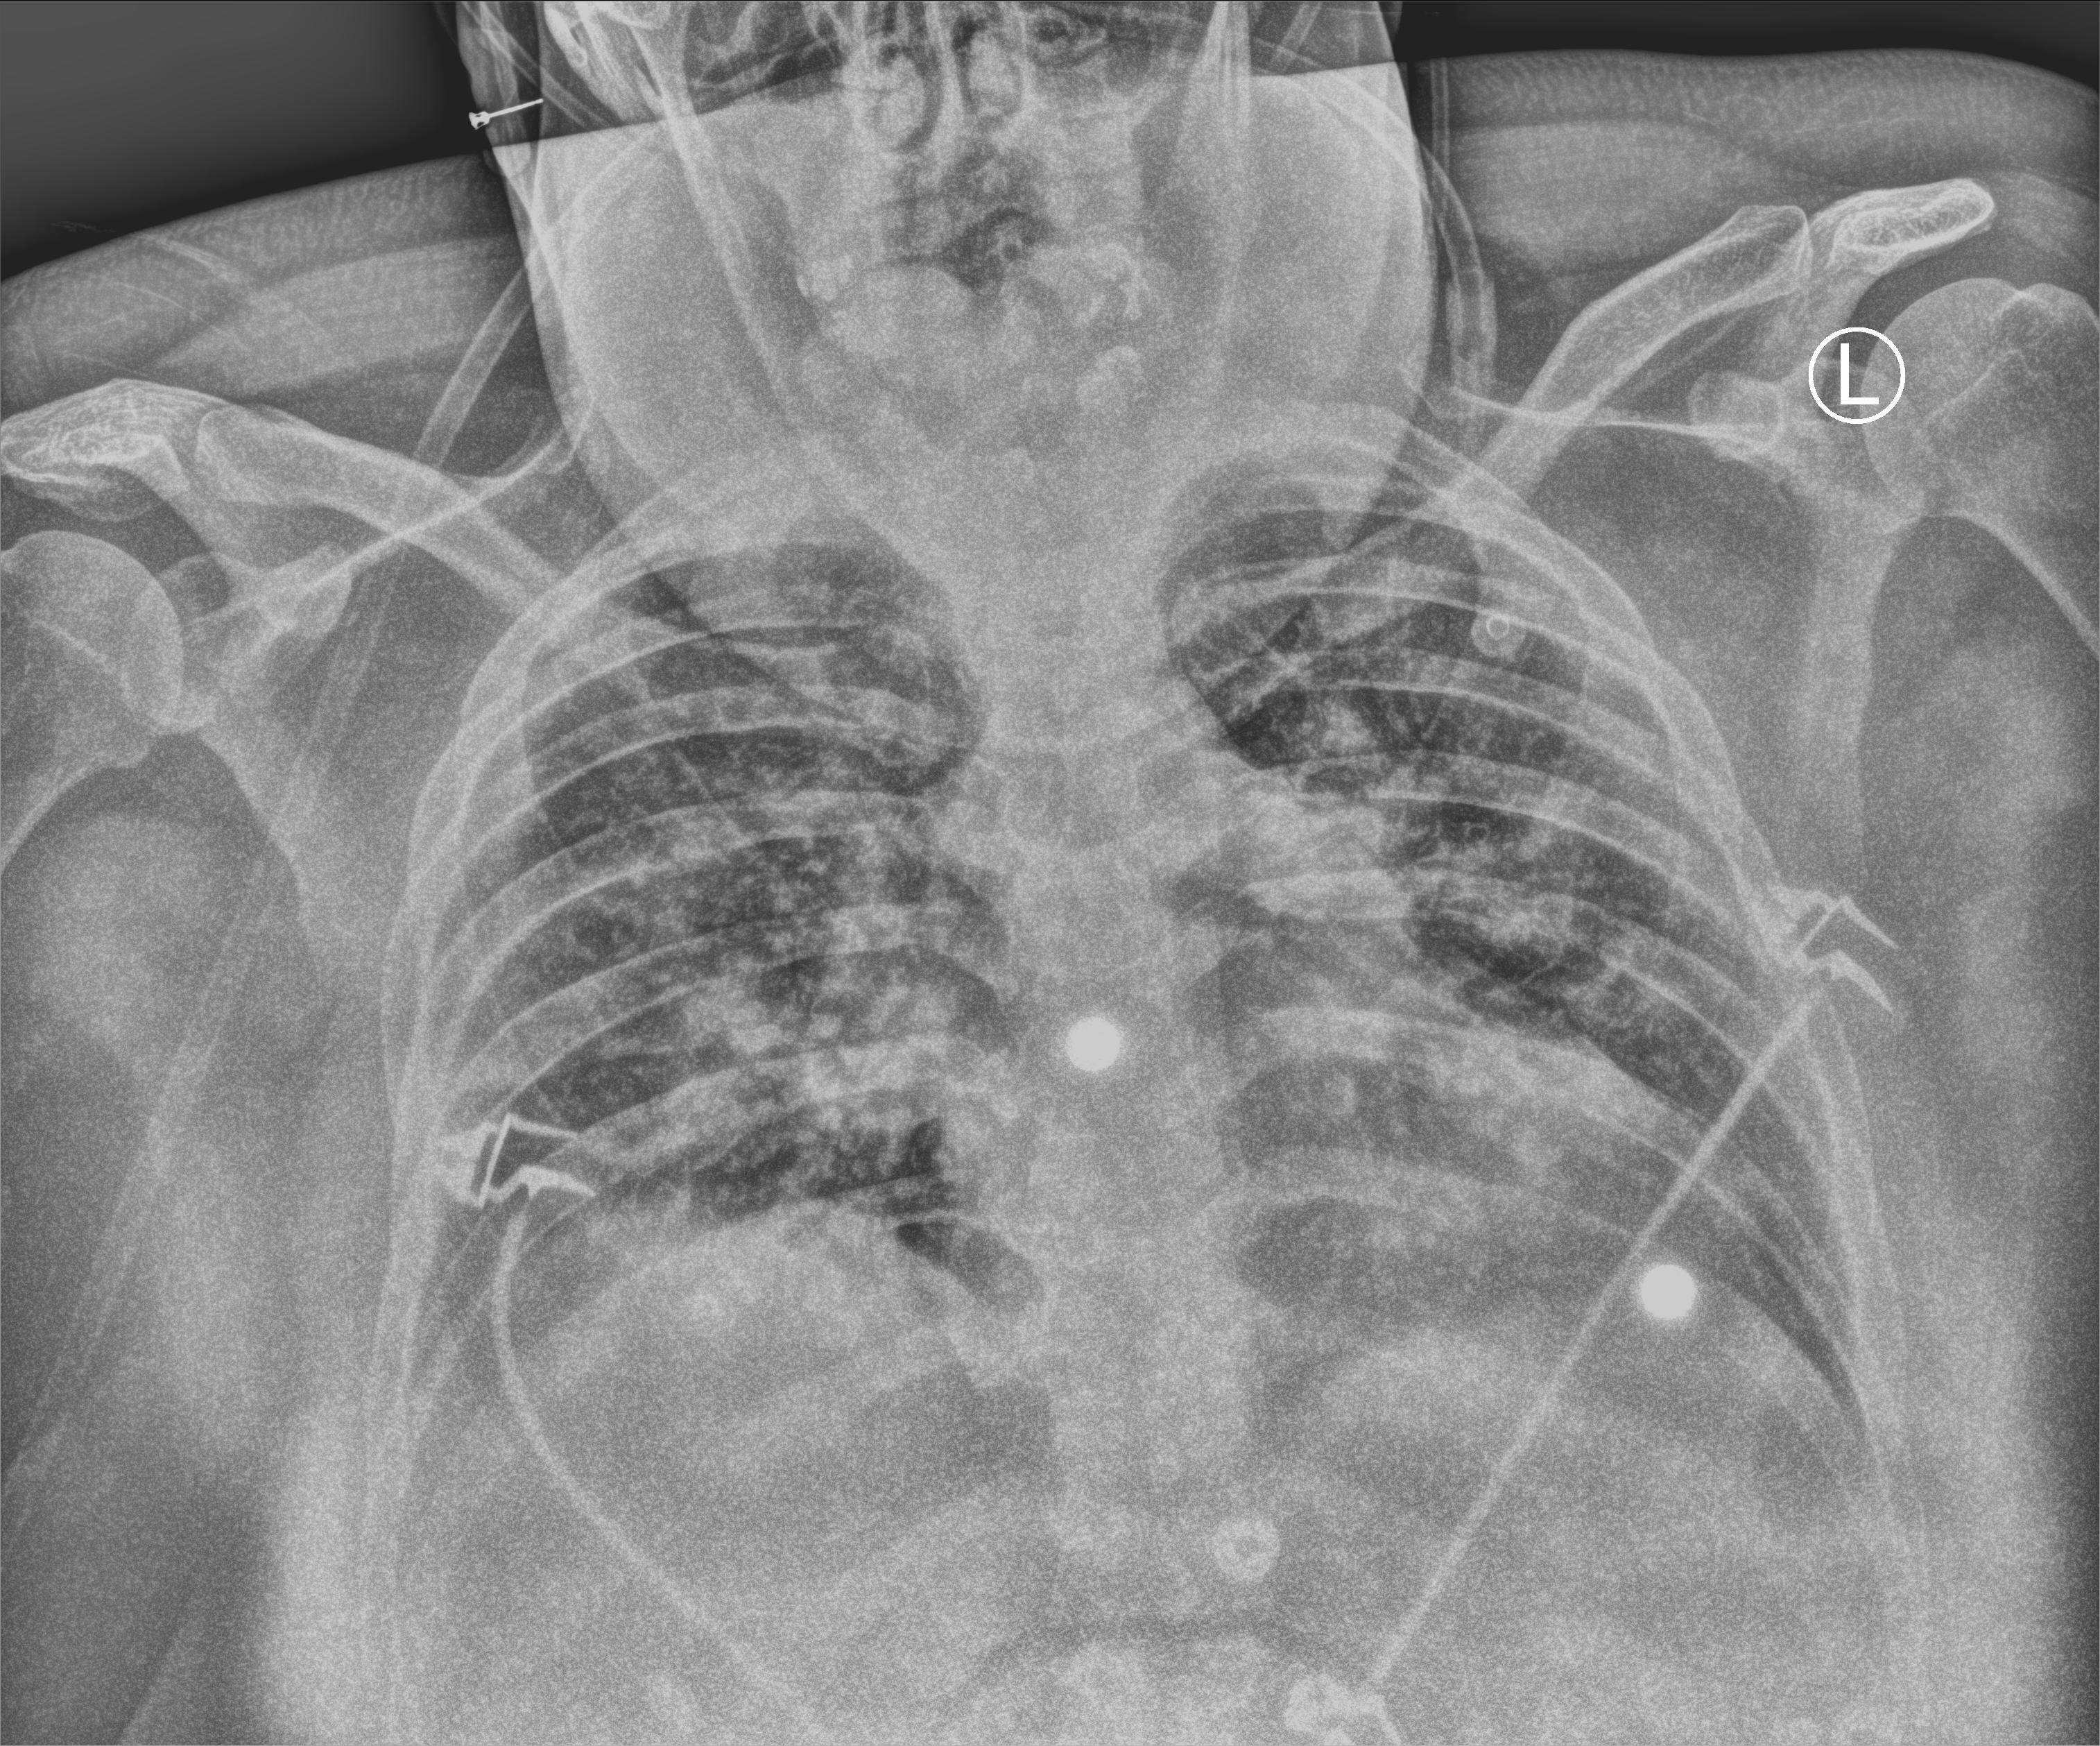
Portable chest radiograph. Female patient hospitalised with COVID-19, age 18–59 years.
Admission-level facts for this patient (not findings on this image; timing relative to this image not recorded):
- mechanically ventilated during this hospital stay: no